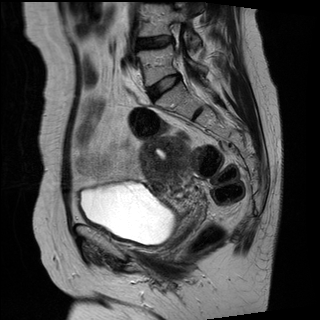
Pelvic MRI for cervical cancer, one sagittal slice. T2-weighted. 1.5 T. TE 89 ms, TR 2740 ms. 4 mm slice thickness. 320 × 320 image matrix. Female patient, age 42 years.
Structures marked on this image (expert manual segmentation):
- uterus and cervix: bounding box [x1, y1, x2, y2] px = [141, 137, 188, 188]